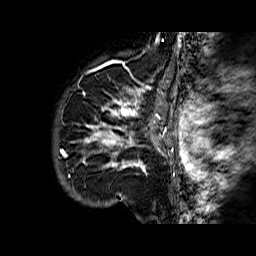
Breast MRI (dynamic contrast-enhanced), one sagittal slice. Slice 53 of 60 in the series (ordered by position). Dynamic contrast-enhanced series, time point 2 of 6 at this slice position (early post-contrast). 1.5 T. TE 6.3 ms, TR 32.4 ms. 4 mm slice thickness. 256 × 256 image matrix. Female patient. From the clinical record (not read from this slice): setting: breast cancer imaged before/during neoadjuvant chemotherapy; receptor status: HR-positive, HER2-negative.
Structures marked on this image (semi-automatic segmentation, software-assisted and operator-edited):
- analysis volume of interest (the breast-tissue region the enhancement analysis was run in; not a lesion): box from (x=68, y=72) to (x=177, y=183) px
- tumour enhancement mask (voxels above the 100 % enhancement threshold inside the analysis volume of interest): (x=82, y=87)–(x=174, y=172)